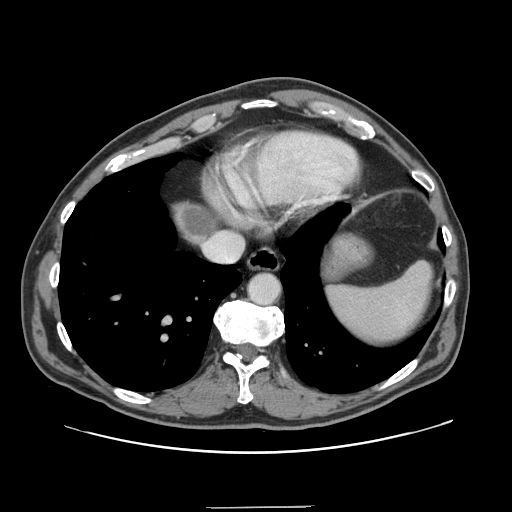
Contrast-enhanced abdominal CT, one axial slice; position 132 of 139 along the scan axis; intravenous contrast given; soft-tissue window (W 400 / L 40 HU); 2.5 mm slice thickness; 512 × 512 image matrix, field of view 397 × 397 mm. Male patient, age 64 years. Case-level facts recorded for this patient, not image findings: diagnosis: colorectal cancer liver metastases, imaged before liver resection; multiple liver metastases: yes; largest metastasis: 3.5 cm.
Structures marked on this image (expert manual segmentation):
- liver: bounding box (x1, y1, x2, y2) in pixels: (176, 205, 215, 243)
- liver metastasis: (184, 209, 214, 240)